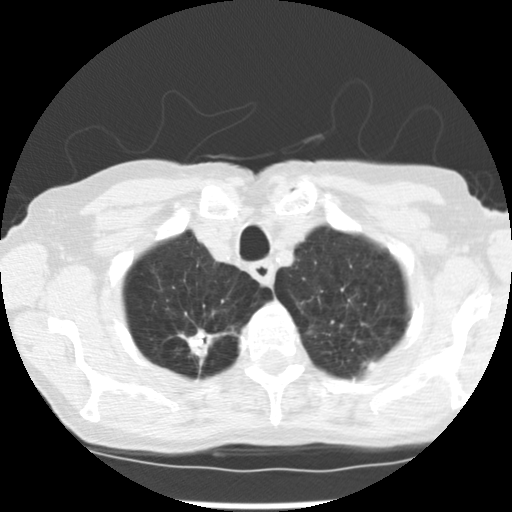
Low-dose screening chest CT, axial slice; first (baseline) screen; lung window (W 1500 / L -600 HU); slice 29 of 265 in the series; 512 × 512 image matrix, field of view 300 × 300 mm. Female, age 72 years at enrolment. Current smoker at enrolment.
Lesion marked by an expert reader, box from (x=174, y=314) to (x=231, y=357) px. The screening reader recorded 3 non-calcified nodules or masses ≥4 mm on this exam; which of them this box marks is not recorded. Official screen result: positive, change unspecified: nodule(s) >= 4 mm or enlarging nodule(s), mass(es), or other non-specific abnormalities suspicious for lung cancer. Later outcome: lung cancer diagnosed 50 days after this screen — adenocarcinoma, NOS, right upper lobe, moderately differentiated (G2), stage IB (AJCC 6th edition), 22 mm at pathology.